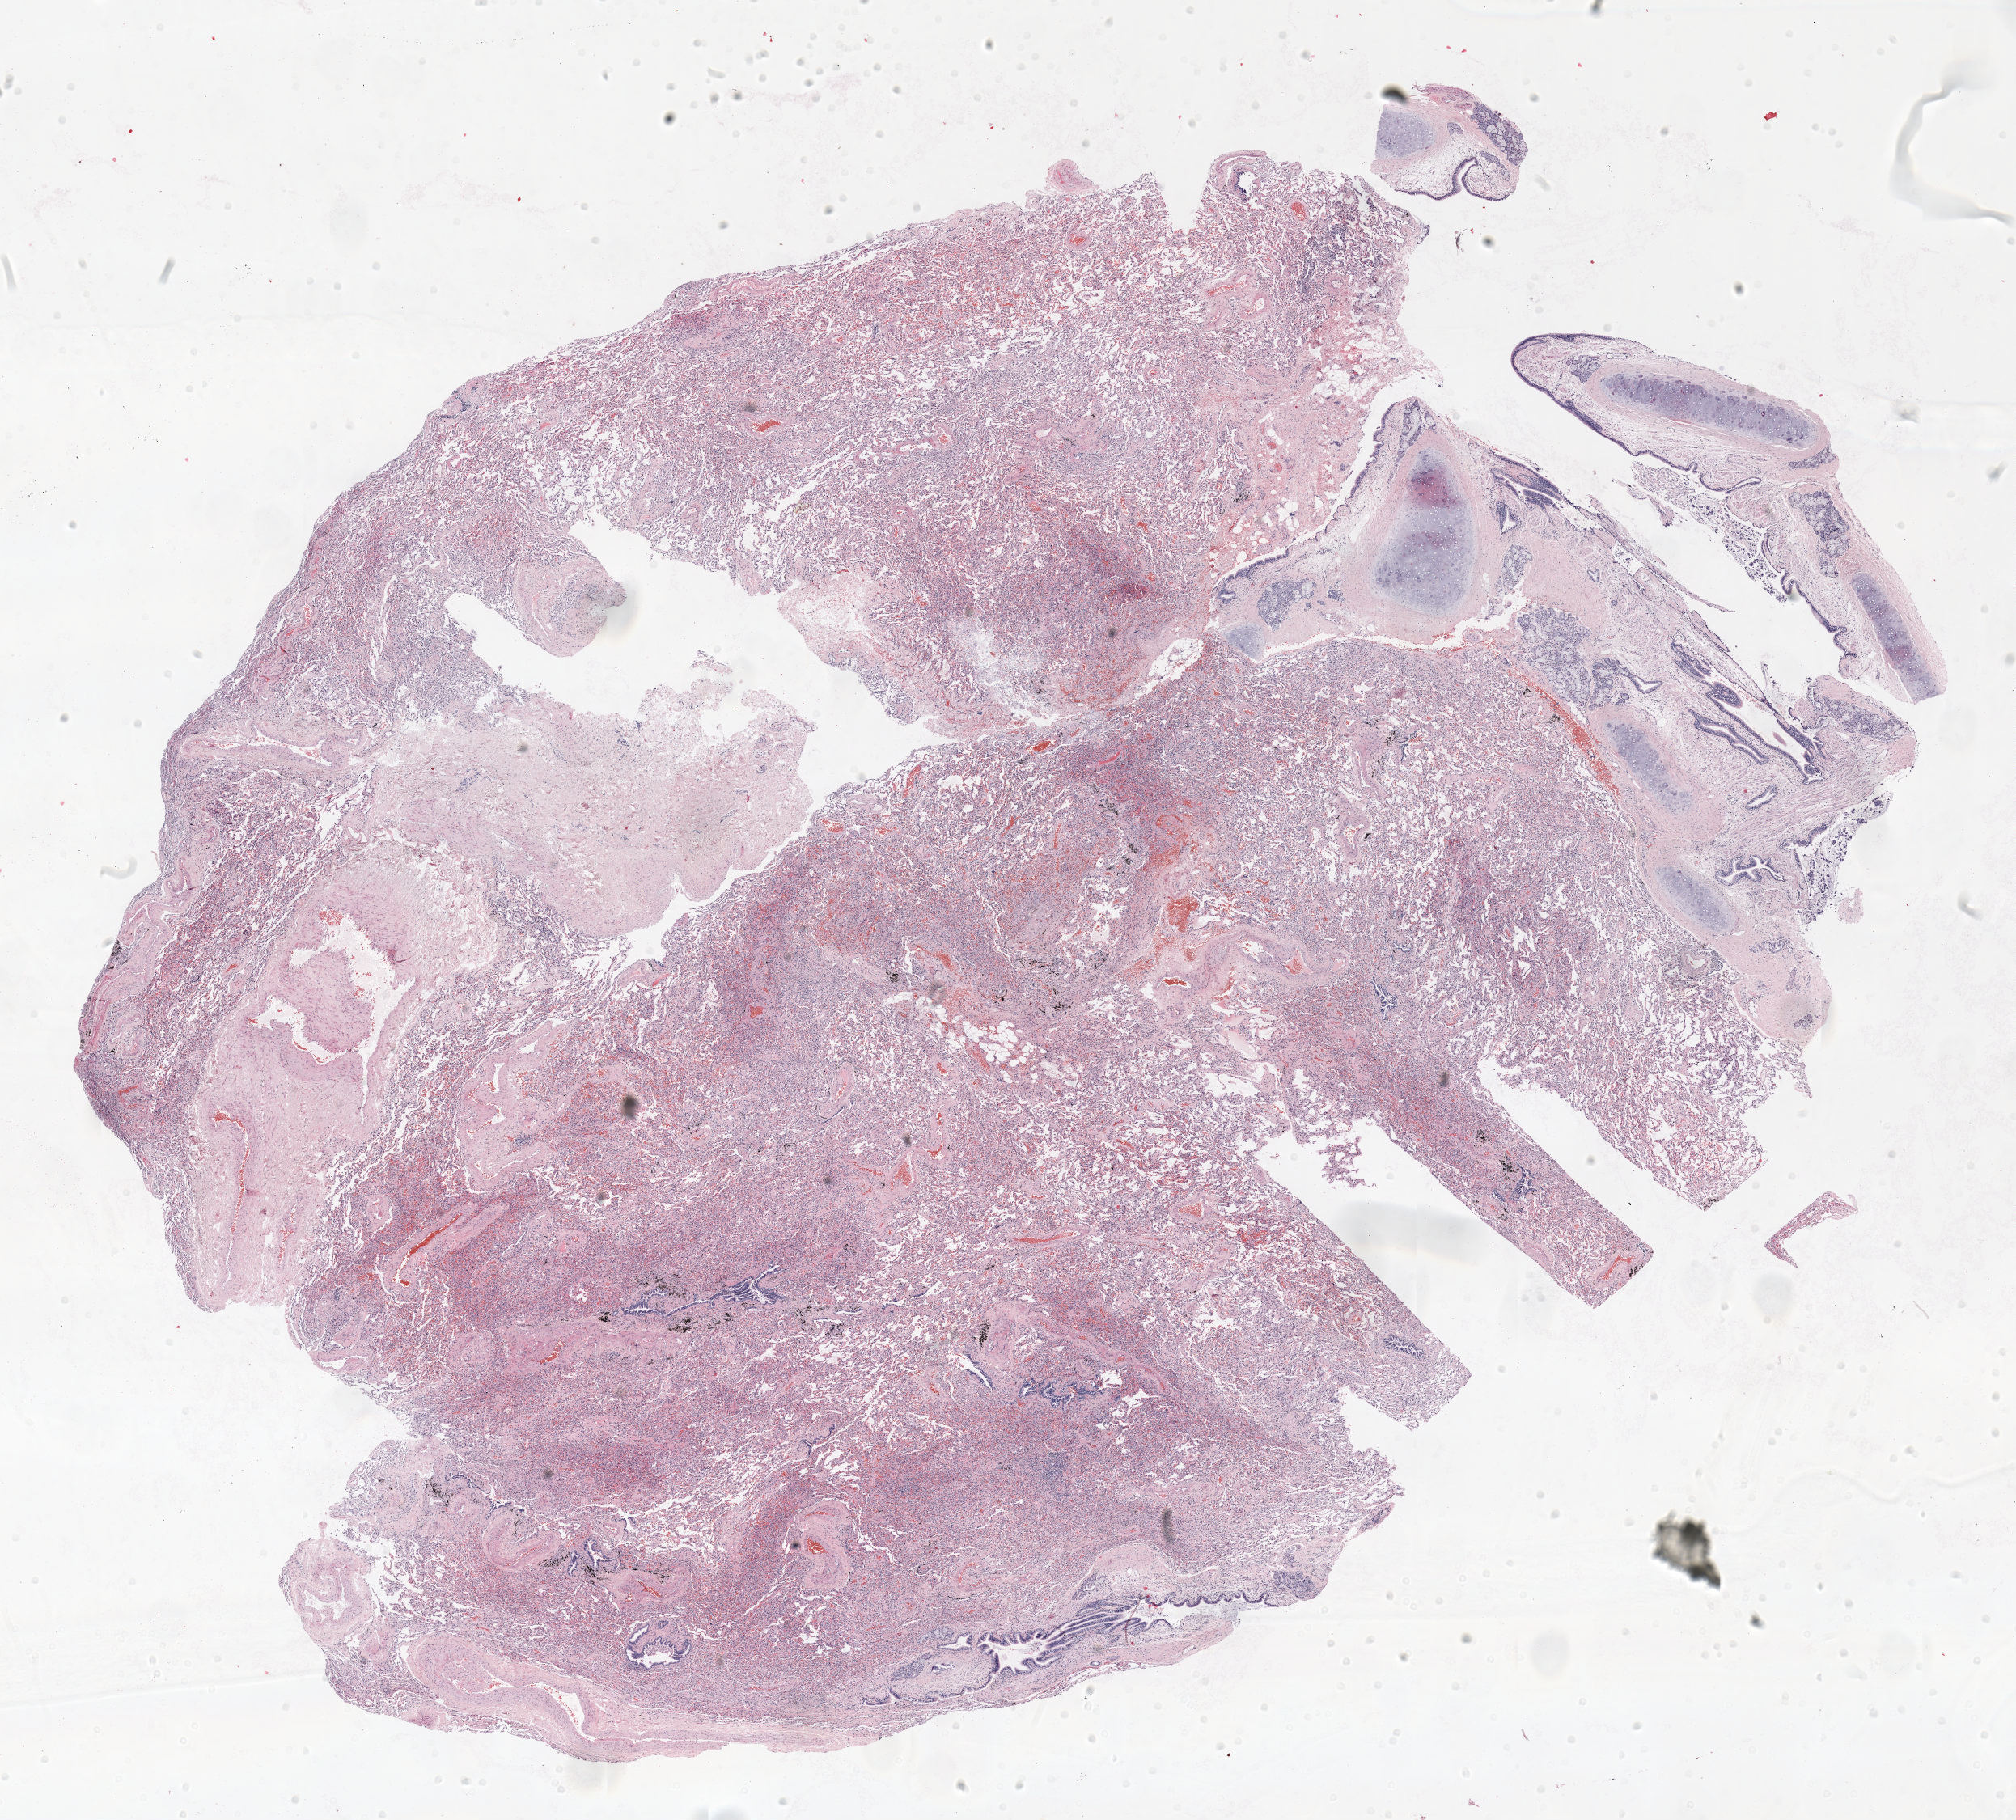
Hematoxylin and eosin (H&E) stained whole-slide image — whole scanned area (about 20.0 x 18.1 mm, from a 20x scan) shown as a low-resolution overview. Formalin-fixed paraffin-embedded (FFPE) section. Lung. Female patient, aged 59 at enrolment. Former smoker at enrolment.
Participant's lung-cancer diagnosis: Bronchiolo-alveolar adenocarcinoma, NOS (ICD-O-3 8250/3).